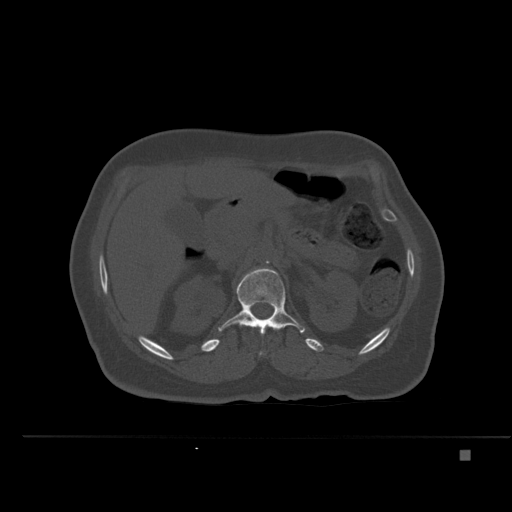
CT including the spine, one axial slice. Position 236 of 477 along the scan axis. Bone window (W 1800 / L 400 HU). 1.5 mm slice thickness. 512 × 512 image matrix, field of view 422 × 422 mm. Patient: female, 74 years. From the clinical record (not read from this slice): primary cancer: colon.
Annotated regions visible in this slice (semi-automatic segmentation, software-assisted and operator-edited):
- L1 vertebra: bounding box (x1, y1, x2, y2) in pixels: (218, 268, 305, 335)
- T12 vertebra: (252, 326, 276, 355)